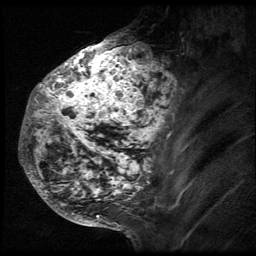
Breast MRI (dynamic contrast-enhanced), one sagittal slice. Position 22 of 64 along the scan axis. 3 images stored at this slice position (order not interpretable as contrast timing). 1.5 T. TE 4.2 ms, TR 9 ms. 2.5 mm slice thickness. 256 × 256 image matrix. Female patient, age 50 years. Case-level facts recorded for this patient, not image findings: setting: breast cancer imaged before/during neoadjuvant chemotherapy; receptor status: triple-negative.
Annotated regions visible in this slice (semi-automatic segmentation, software-assisted and operator-edited):
- analysis volume of interest (the breast-tissue region the enhancement analysis was run in; not a lesion): bounding box (x1, y1, x2, y2) in pixels: (24, 39, 193, 212)
- tumour enhancement mask (voxels above the 140 % enhancement threshold inside the analysis volume of interest): (24, 39, 192, 209)